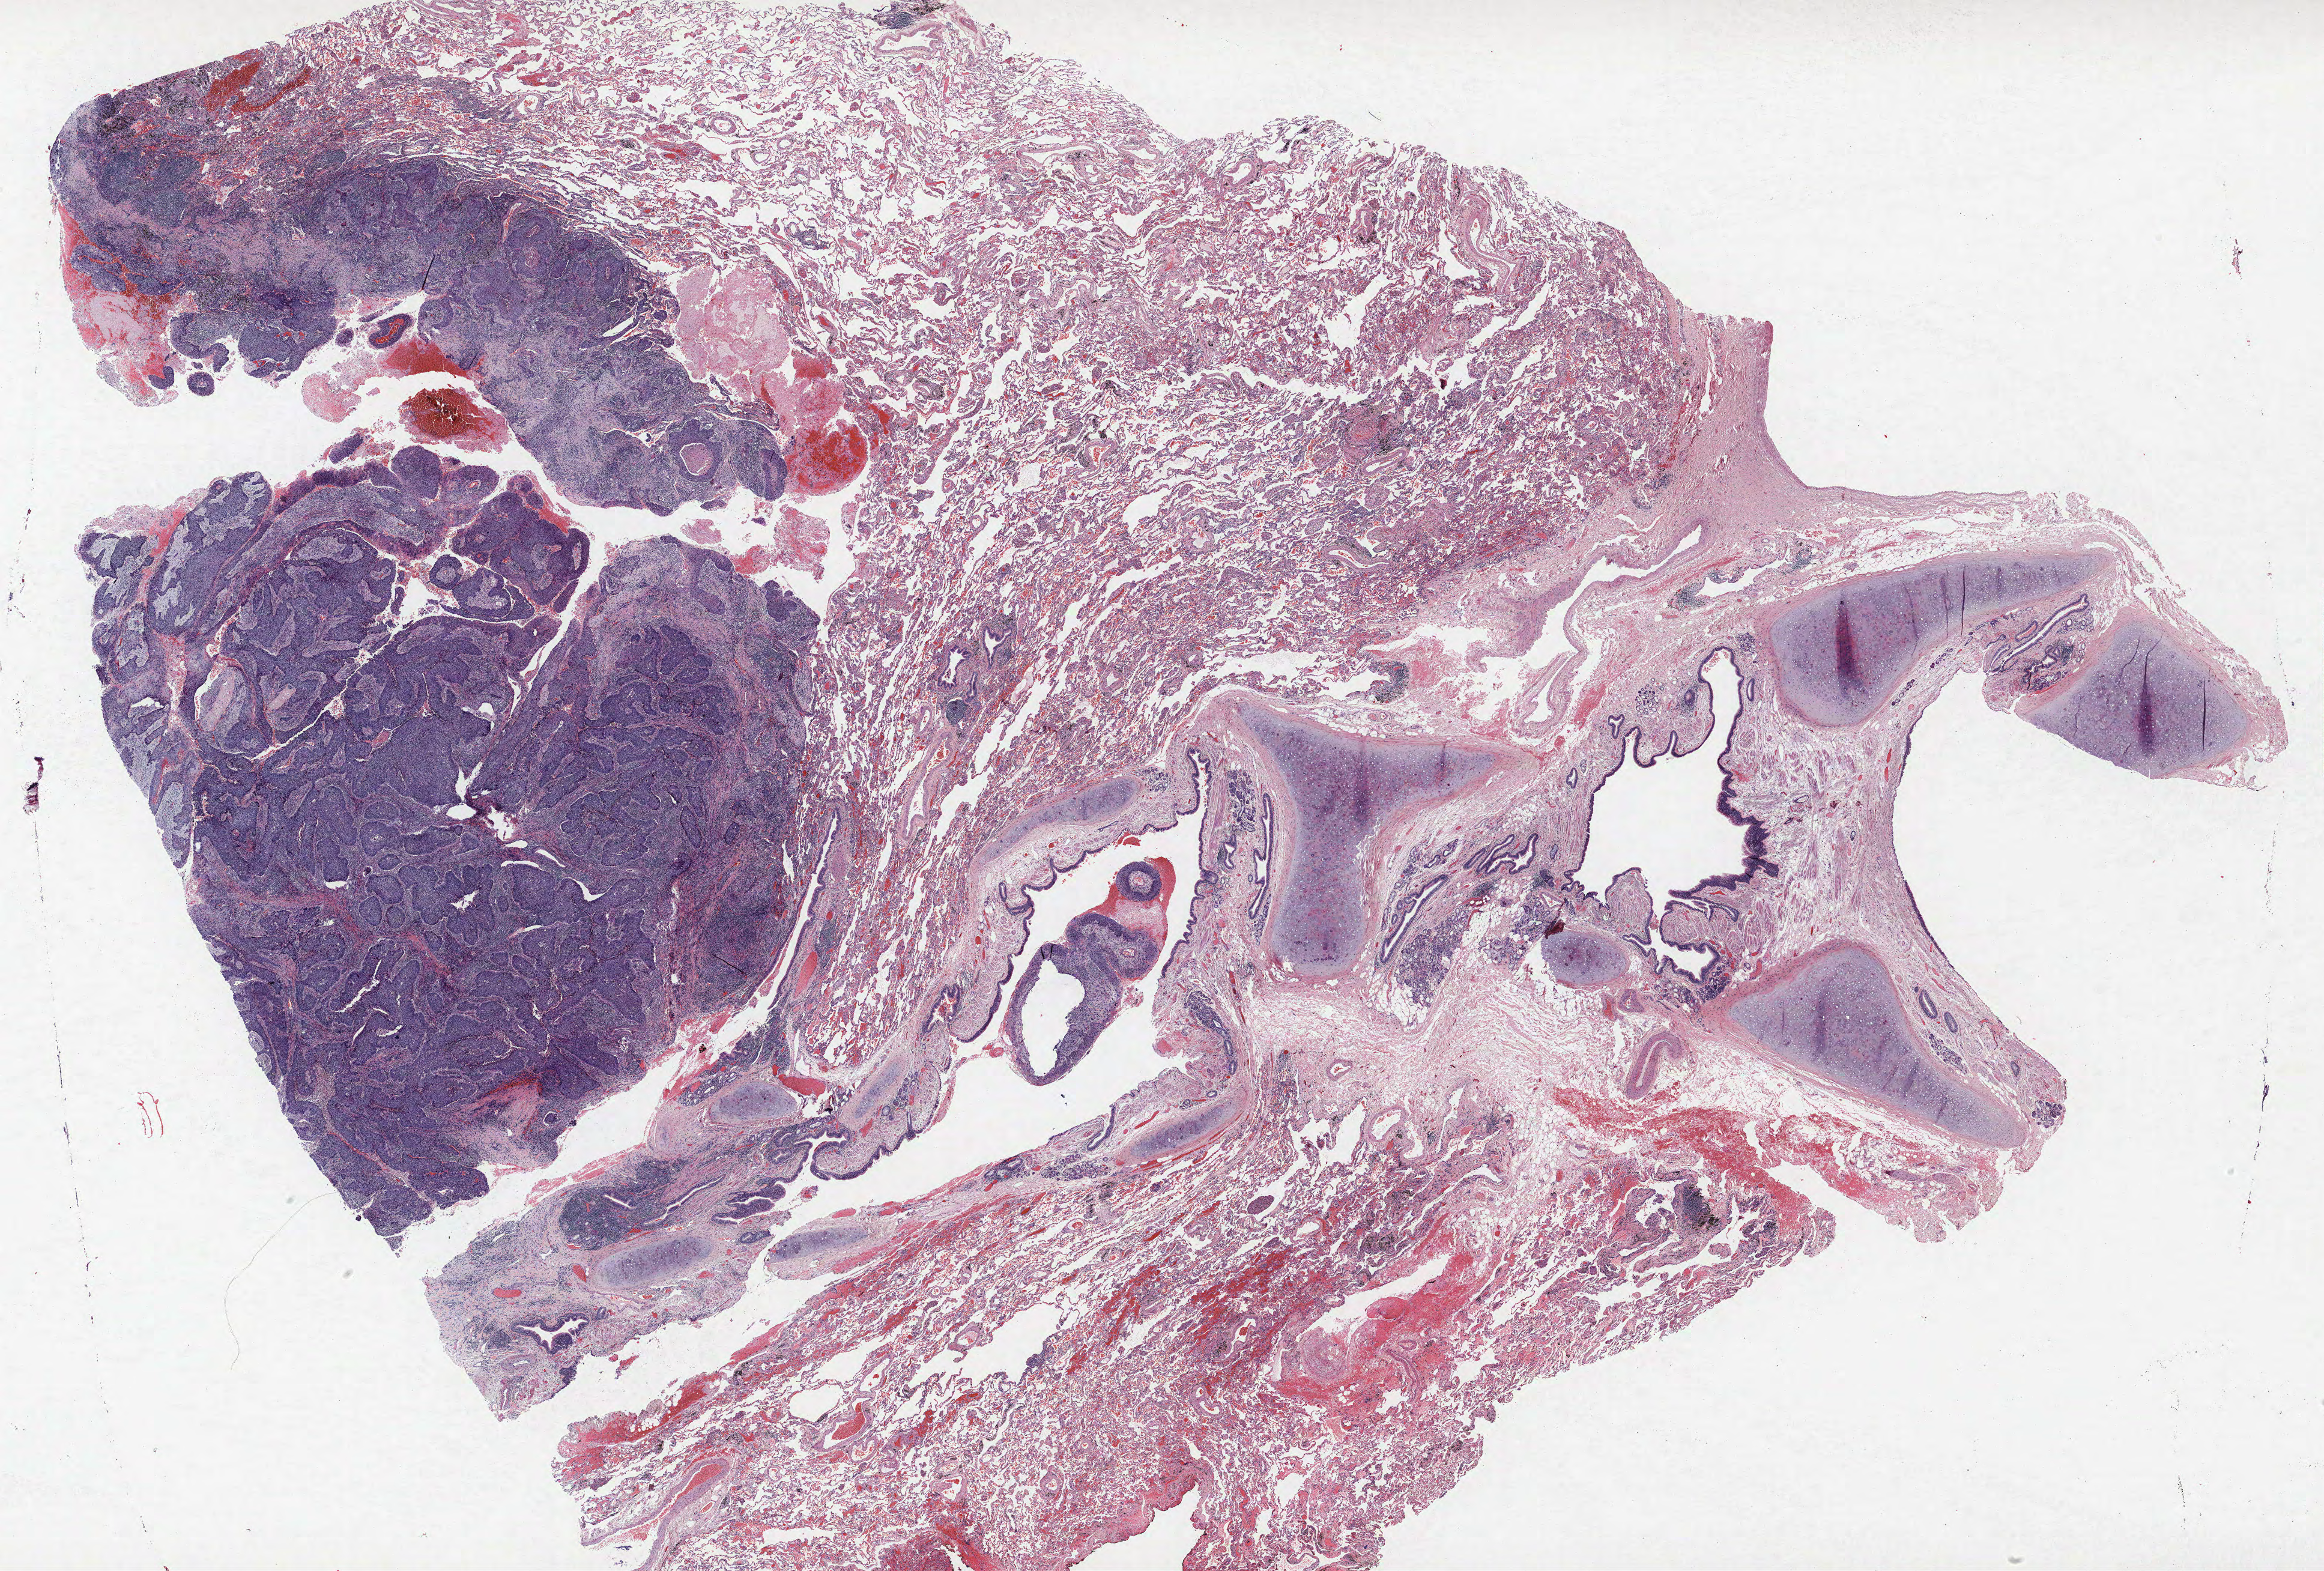
H&E-stained whole-slide image — a low-resolution overview of the entire scanned area, about 31.0 x 20.9 mm. FFPE section. Lung tissue. Male, age 67 at enrolment. Grade: poorly differentiated (G3).
• participant's lung-cancer diagnosis: Squamous cell carcinoma, NOS (ICD-O-3 8070/3)
• ICD-O-3 topography: upper lobe of lung (C34.1)
• tumour size (pathology): 27 mm
• stage (AJCC 6th edition): IA
• primary tumour location (clinical record): right upper lobe
• note: participant had 2 primary lung cancers recorded; fields above describe the first